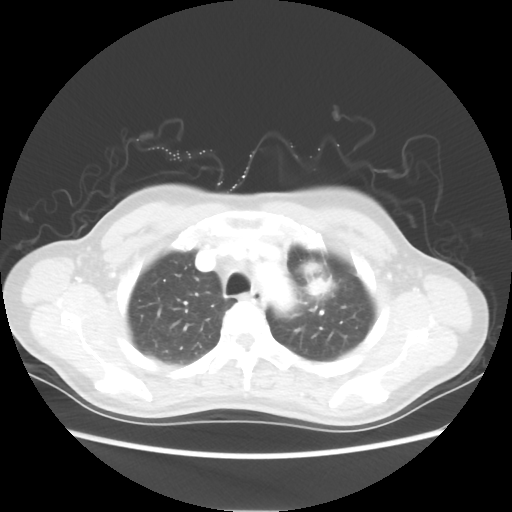
Chest CT, one axial slice; slice 43 of 54 in the series (ordered by position); reconstruction kernel STANDARD; 80 kVp; lung window (W 1500 / L -600 HU); 512 × 512 image matrix. Patient: female, 53 years. Case-level facts recorded for this patient, not image findings: clinical TNM (as recorded): T1c N0 M0.
Outlined on this slice (bounding box drawn by a radiologist):
- lung tumour (recorded histology: adenocarcinoma): bounding box <298,261,333,300> (left, top, right, bottom; pixels)
- lung tumour (recorded histology: adenocarcinoma): <300,256,335,302>